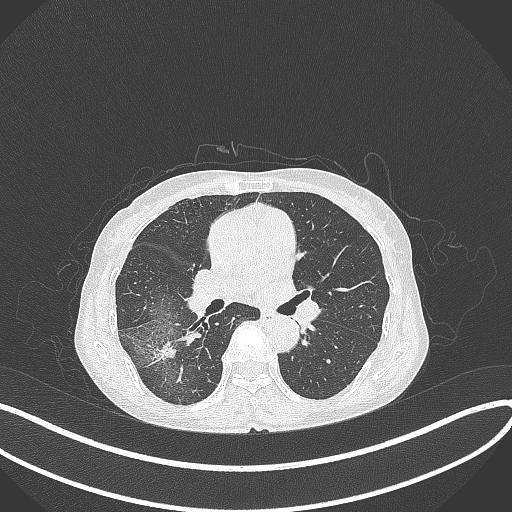
Chest CT, one axial slice; slice 219 of 371 in the series (ordered by position); 120 kVp; lung window (W 1500 / L -600 HU); 512 × 512 image matrix, field of view 400 × 400 mm. Female patient, age 69 years. Case-level facts recorded for this patient, not image findings: clinical TNM (as recorded): T1b N0 M0.
Annotated regions visible in this slice (rectangle marked by the reading radiologist):
- lung tumour (recorded histology: adenocarcinoma): bounding box <151,336,179,365> (left, top, right, bottom; pixels)